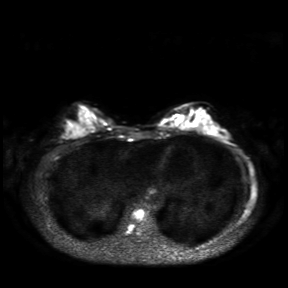
Breast MRI, one axial slice. Position 10 of 30 along the scan axis. Diffusion-weighted series; image 2 of 4 stored at this slice position (different b-values; order by instance number). 3 T. 4 mm slice thickness. 288 × 288 image matrix, field of view 360 × 360 mm. Female patient.
Structures marked on this image (expert manual segmentation):
- tumour on diffusion-weighted imaging: bounding box [x1, y1, x2, y2] px = [170, 116, 176, 121]